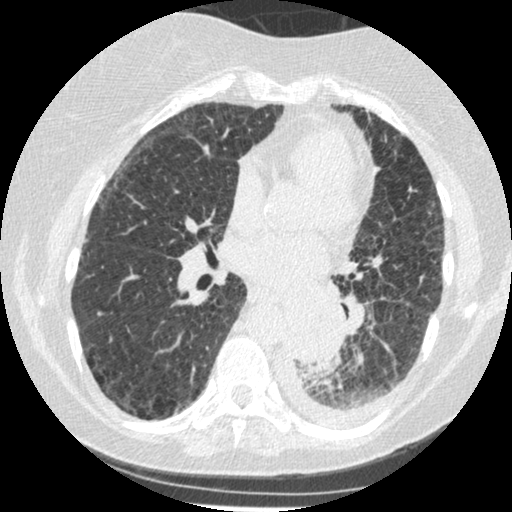
Chest CT (low-dose screening protocol), one axial image; third annual screen; lung window (W 1500 / L -600 HU); 1.25 mm slice thickness; slice 228 of 341 in the series. Female participant, aged 60 years at enrolment. Former smoker at enrolment.
• Lesion marked by an expert reader, box from (x=275, y=304) to (x=343, y=375) px.
• The exam's reader record, not a measurement of the box and not confirmed to be the same lesion: non-calcified nodule or mass ≥4 mm, left lower lobe, 54 × 38 mm, smooth margins, soft tissue attenuation, pre-existing on the prior screen: yes; interval growth: yes.
• Participant outcome: lung cancer diagnosed 15 days after this screen — small cell carcinoma, NOS, left lower lobe, undifferentiated (G4), stage IV (AJCC 6th edition), 69 mm at pathology.